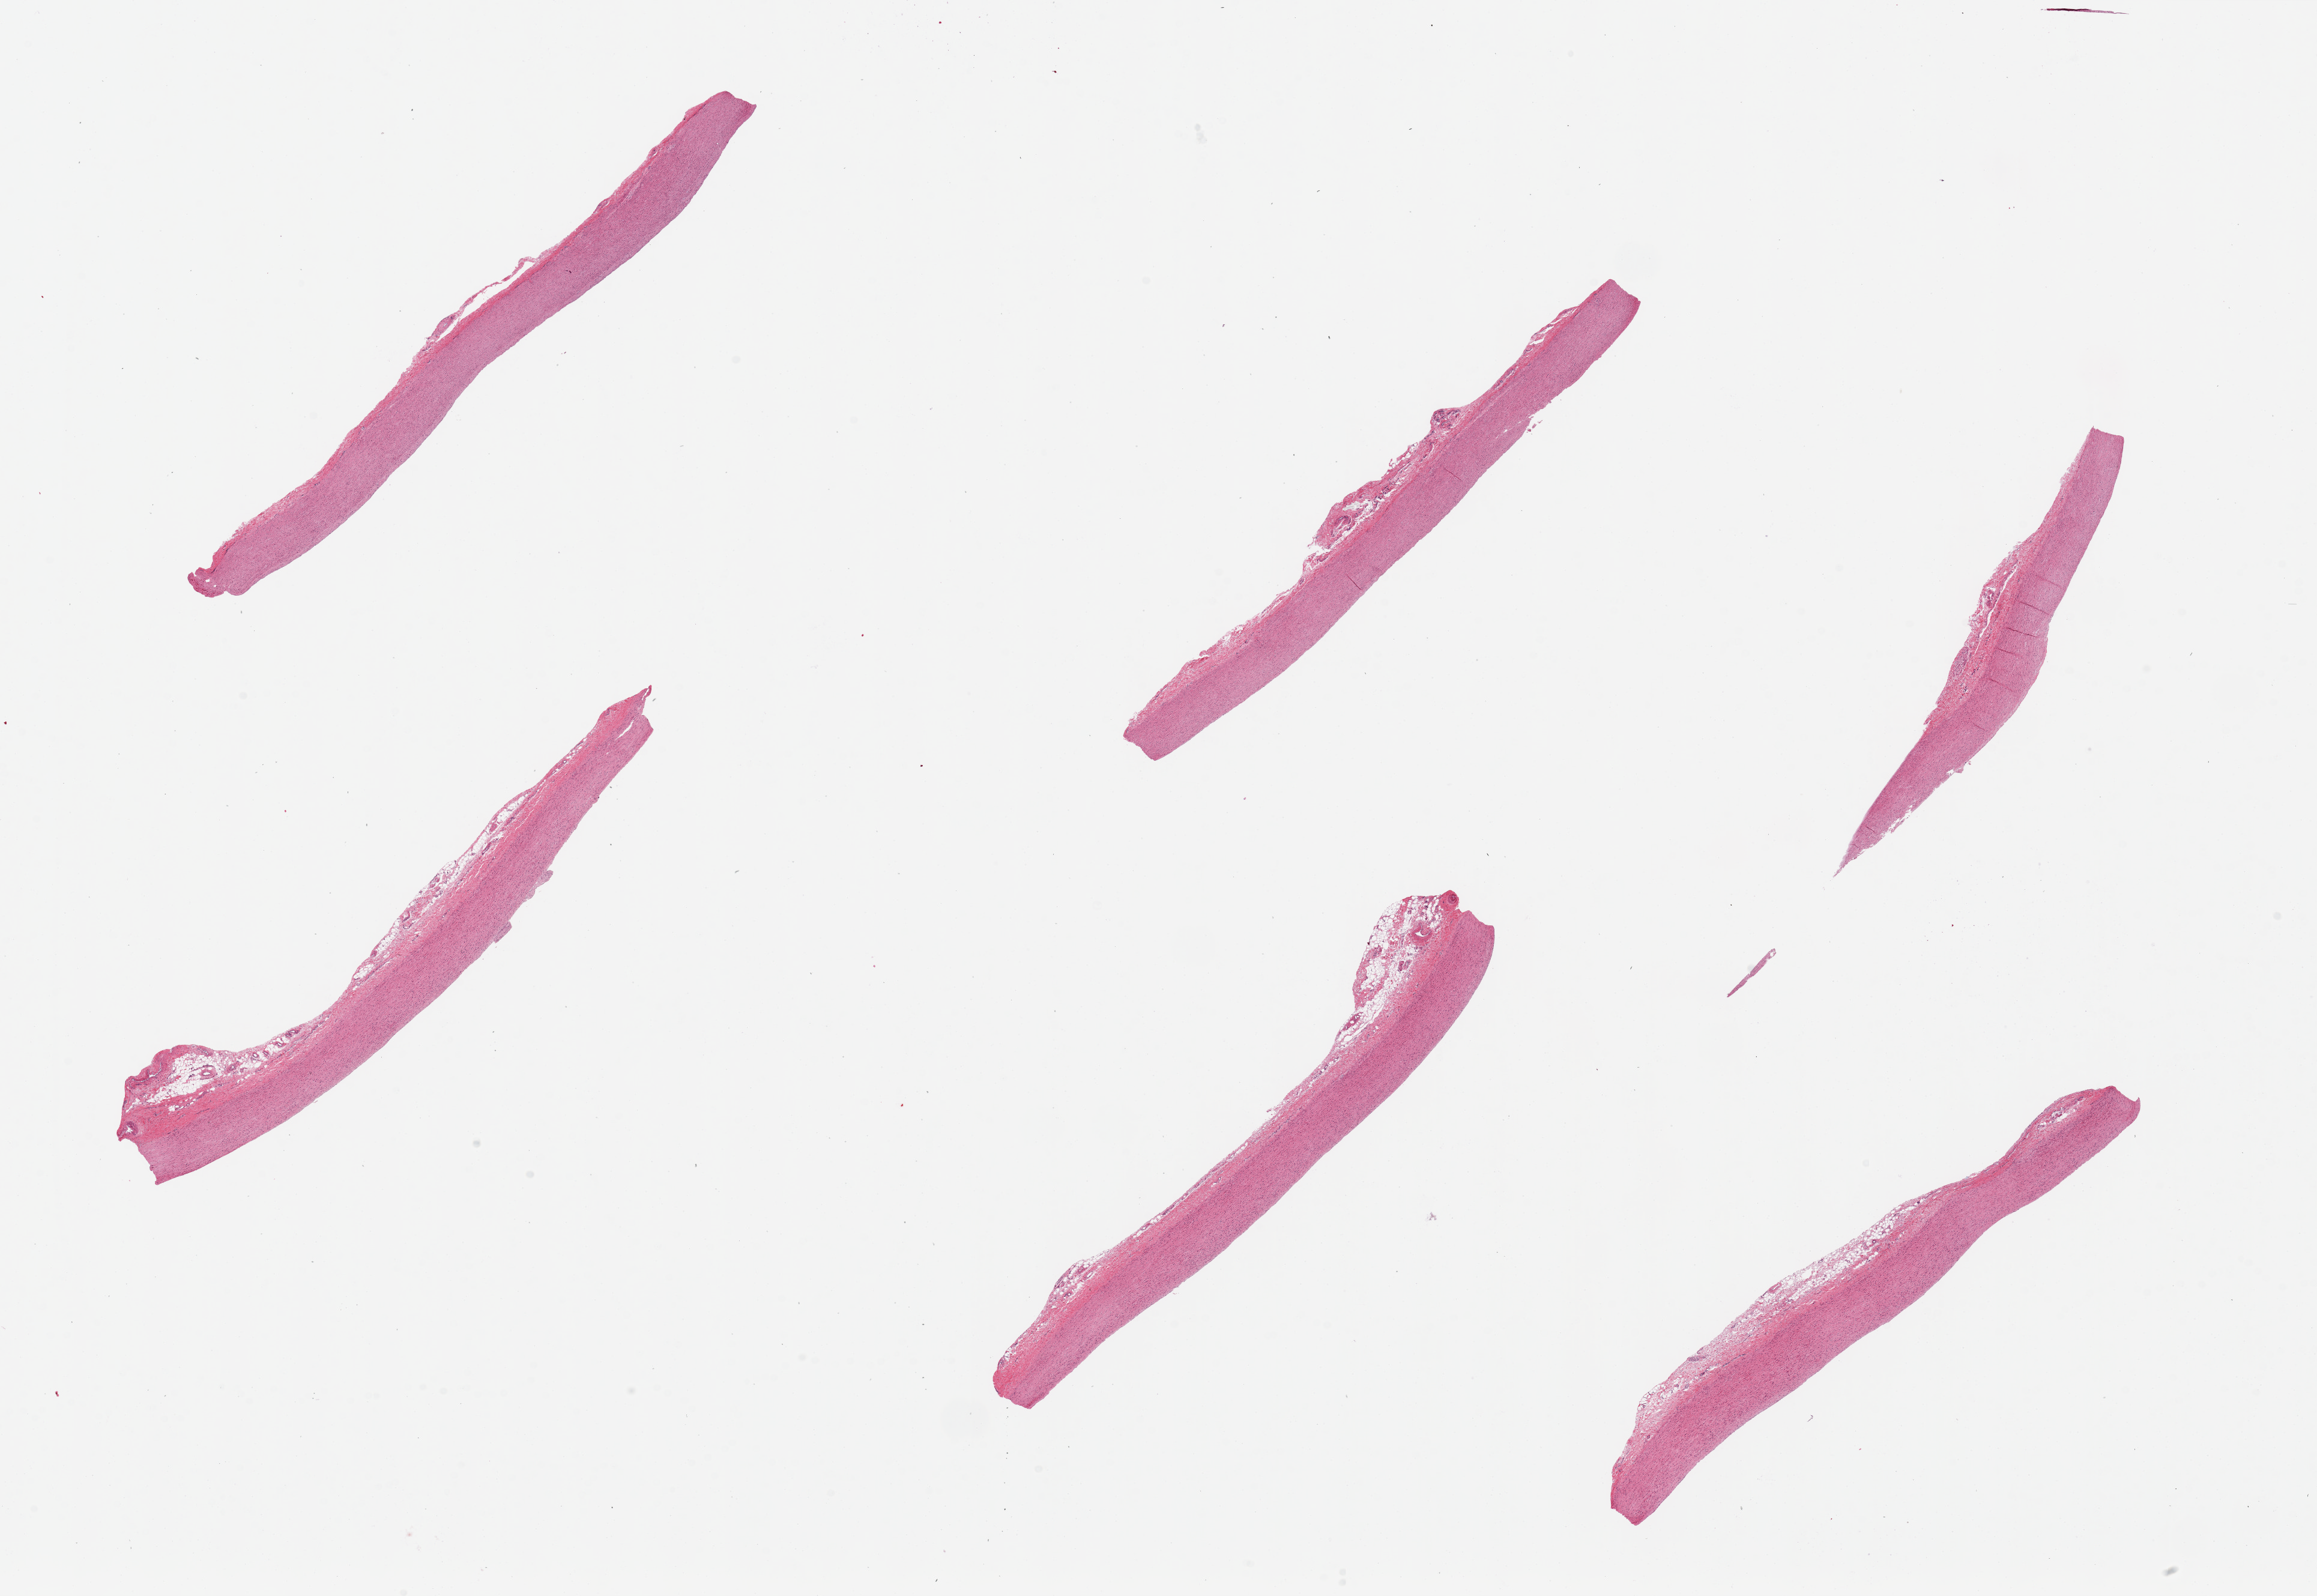
H&E whole-slide image, whole scanned area (about 30.5 x 21.0 mm) shown as a low-resolution overview. PAXgene-fixed, paraffin-embedded tissue. Target tissue: aorta. Tissue donor sample. Female donor.
Pathologist's review note for this sample: 6 pieces, up to 10mmx807um; focal periadventitial adipose.